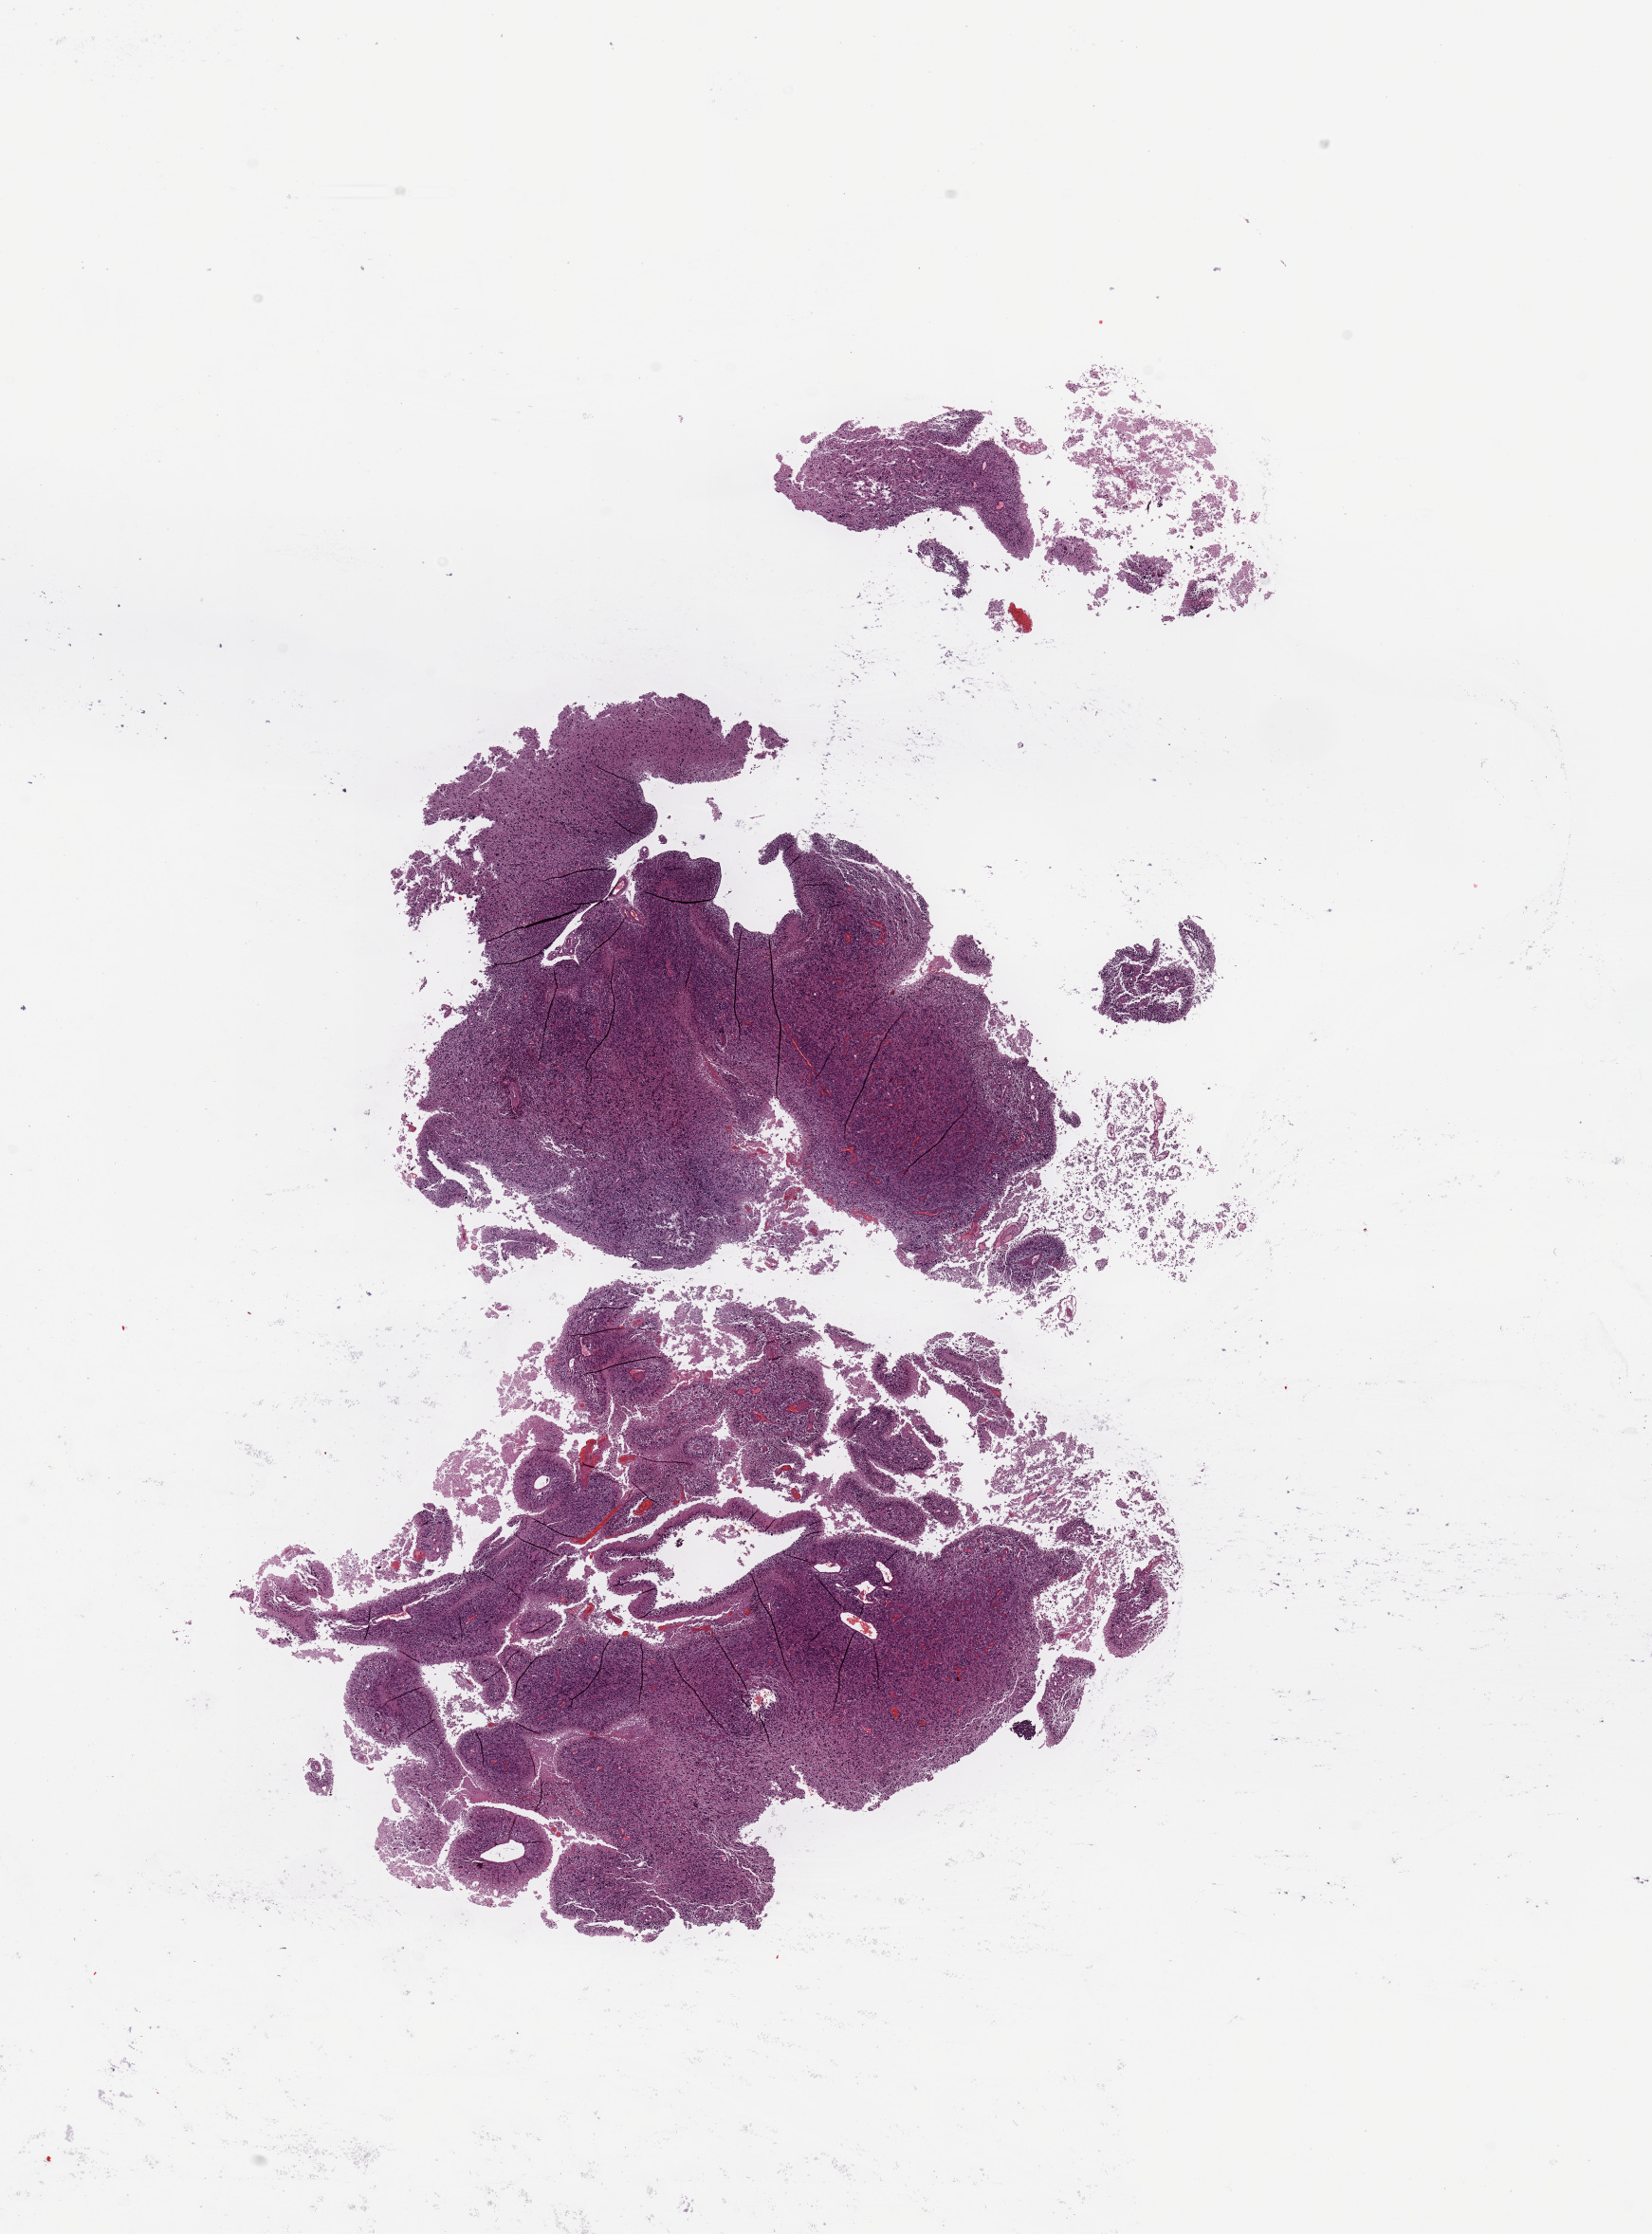
Digitized H&E-stained tissue section (whole slide) — shown as a low-resolution overview of the whole scanned area (about 13.8 x 18.6 mm), tumour tissue sample, sampled site: brain. Patient: female, age 61 years. Composition of this section per pathologist review: tumour nuclei 80%, necrosis 10%.
Histologic diagnosis: Glioblastoma. Primary tumour site (as recorded): frontal lobe.